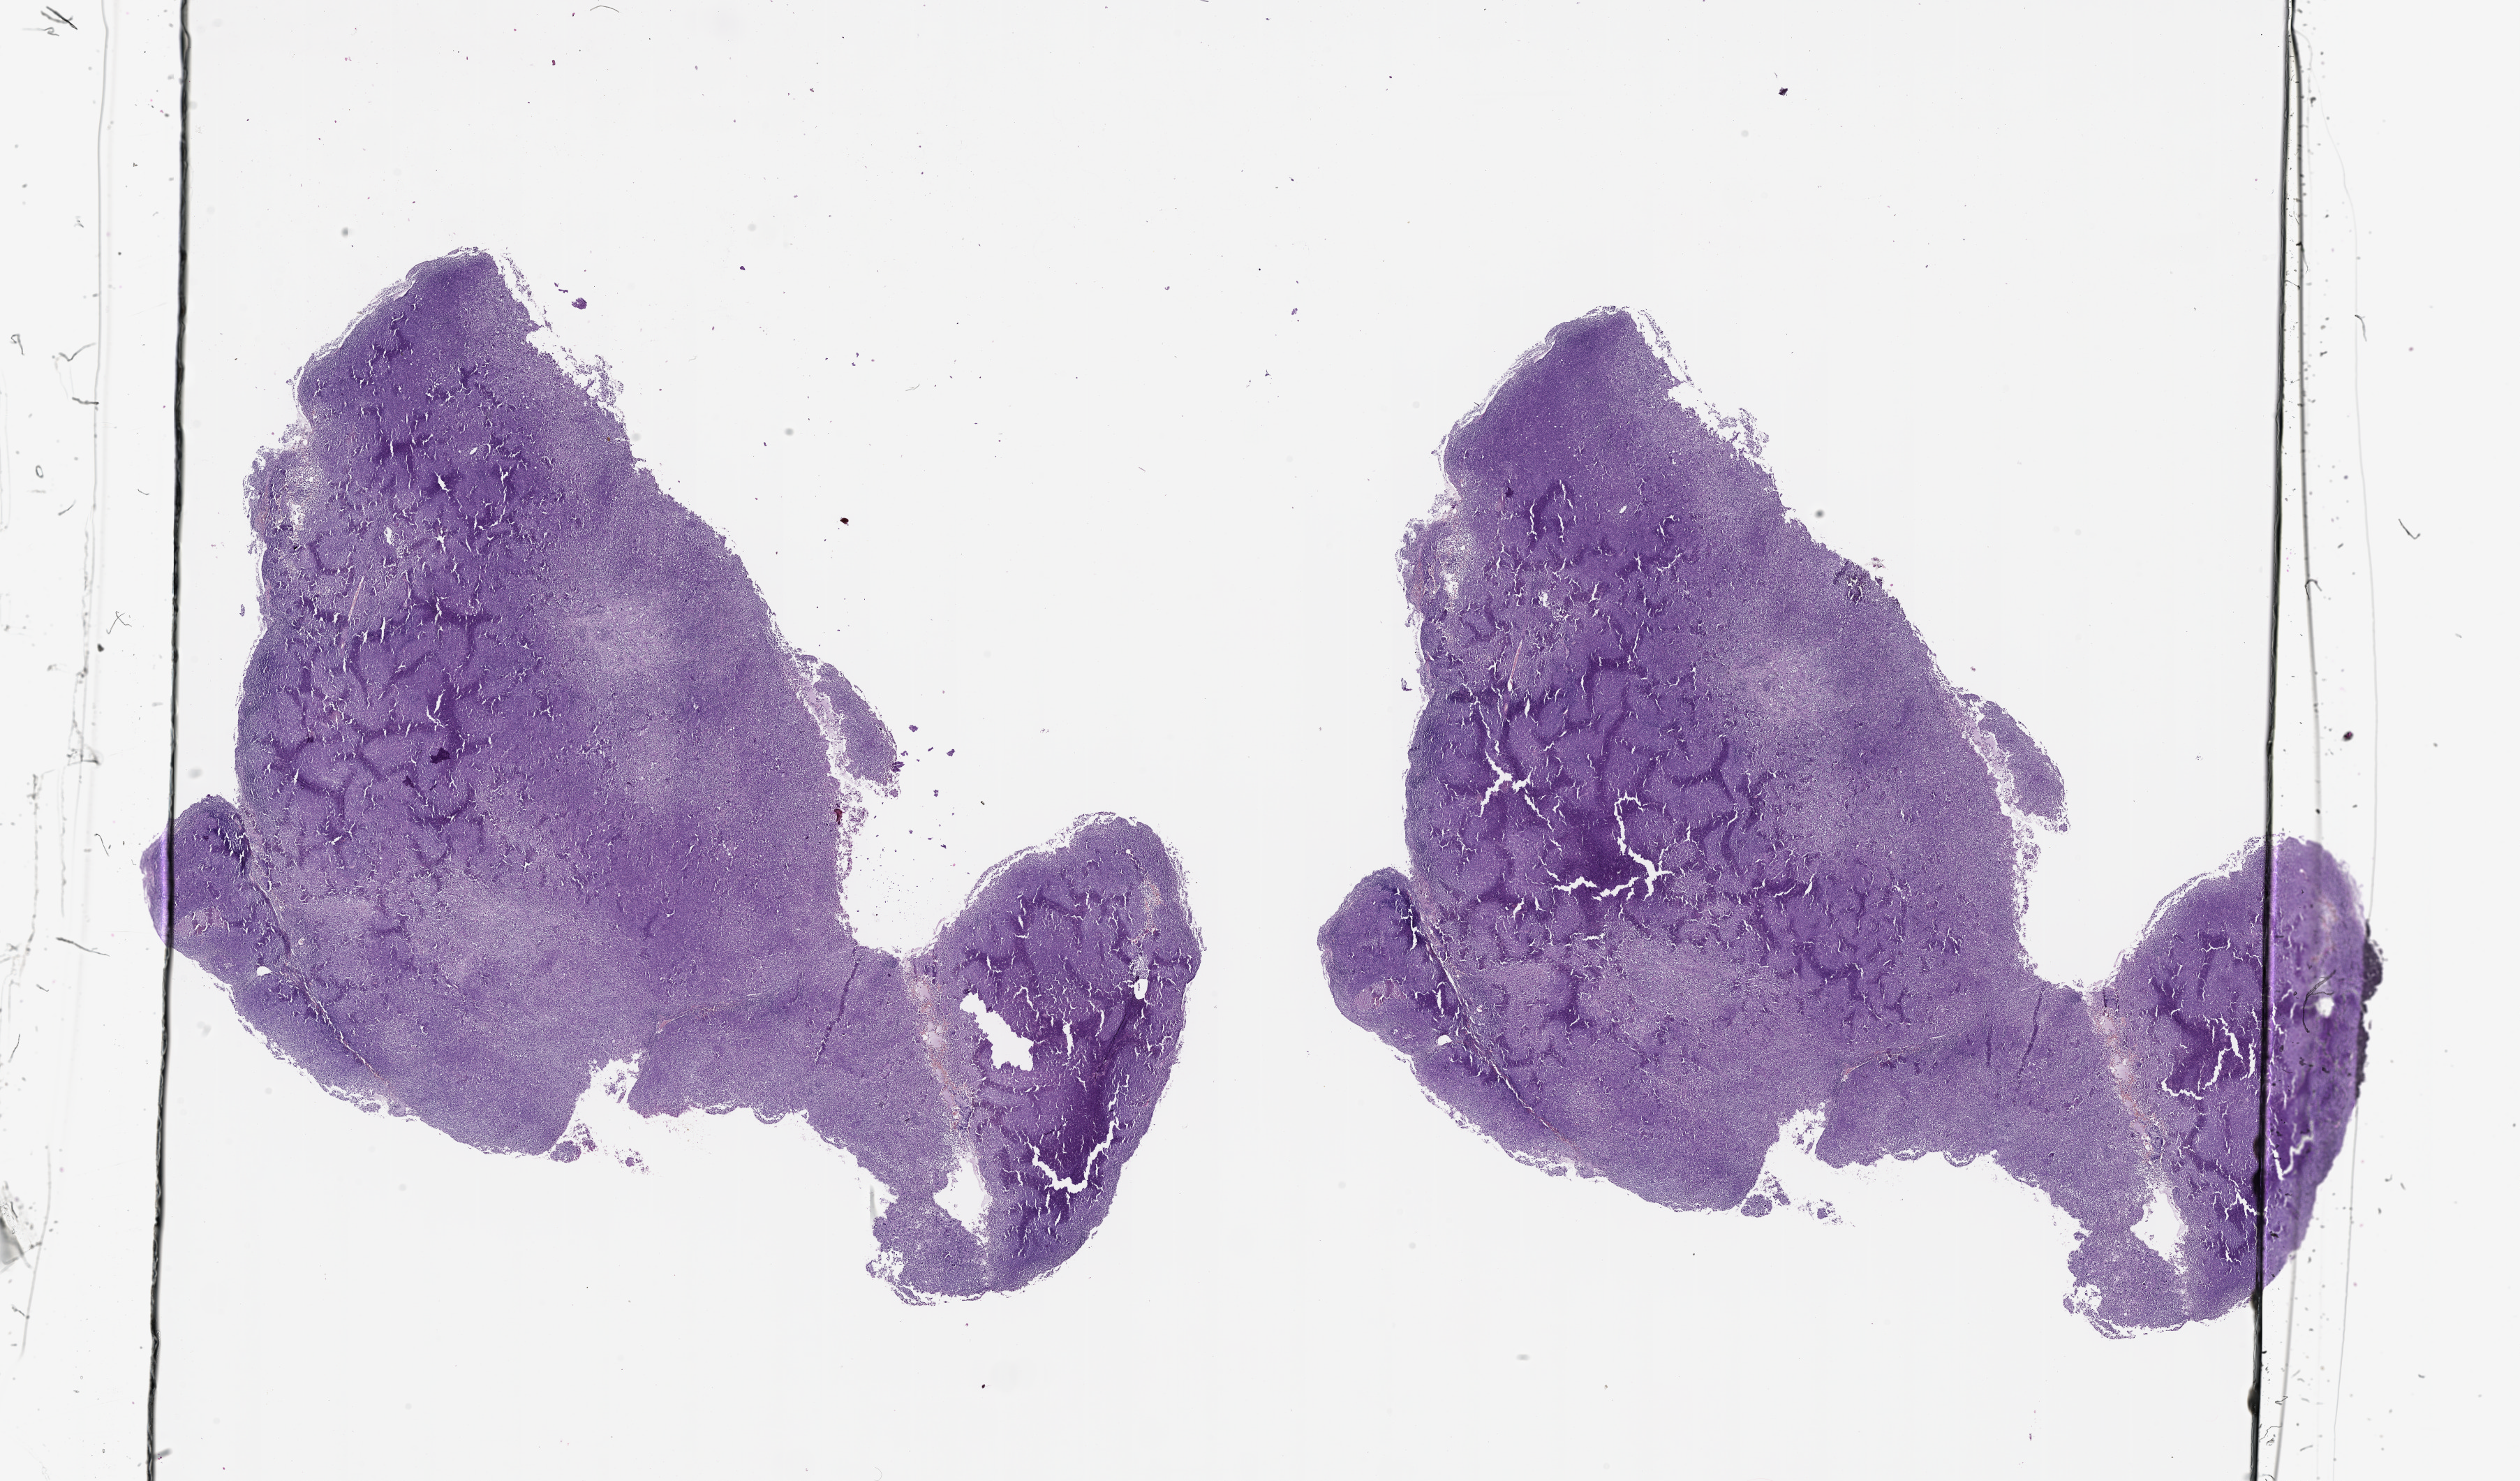
Digitized H&E tissue section (whole slide), a low-resolution overview of the entire scanned area, about 29.1 x 17.1 mm (slide scanned at 20x). Tumour tissue sample, sampled site: trunk. Patient: male, age 47 years. Pathologist review of this section (percent, as recorded): tumour nuclei 80%, necrosis 0%.
This section: metastatic tumour tissue. Patient diagnosis: Malignant melanoma, NOS.